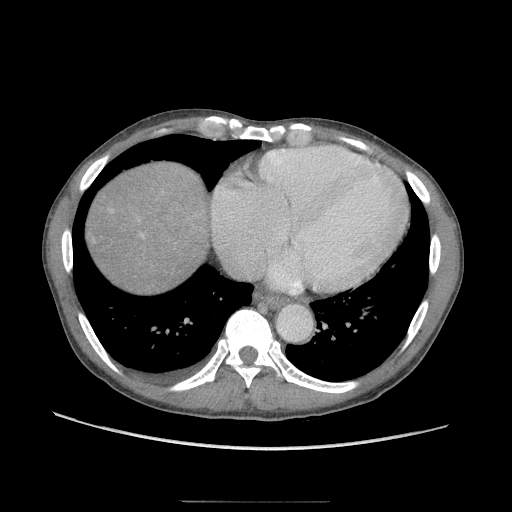
Contrast-enhanced abdominal CT (liver protocol), one axial slice. Position 94 of 103 along the scan axis. Reconstruction kernel STANDARD. Soft-tissue window (W 400 / L 40 HU). 2.5 mm slice thickness. 512 × 512 image matrix. Case-level facts recorded for this patient, not image findings: diagnosis: hepatocellular carcinoma (patient treated with transarterial chemoembolisation; whether this scan precedes or follows treatment is not stated here); TNM stage (as recorded): Stage-IIIA; Child-Pugh class: A; tumour nodularity: multinodular; tumour size: 16 cm.
Structures marked on this image (semi-automatically segmented with operator editing):
- abdominal aorta: box from (x=277, y=304) to (x=311, y=340) px
- liver parenchyma outside the tumour (the mass and vessels are separate outlines, so this box may not span the whole liver): (x=89, y=162)–(x=211, y=289)